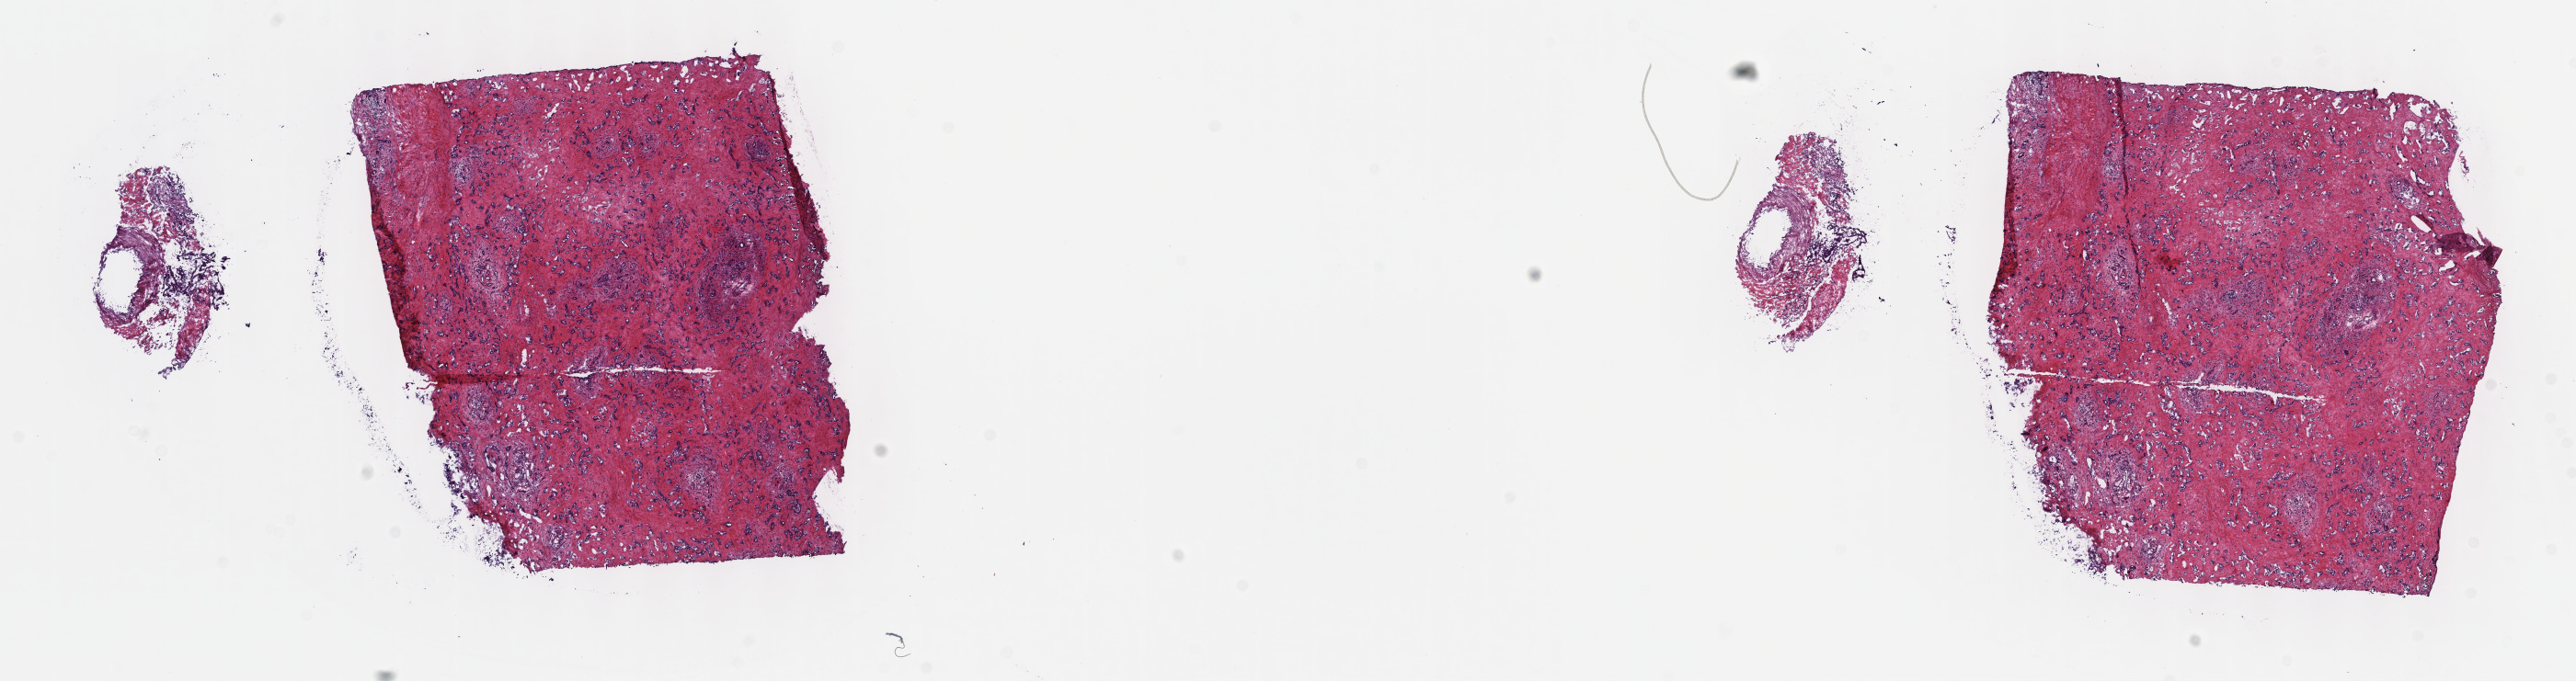
Whole-slide histology image, Hematoxylin and eosin (H&E) stained, shown as a low-resolution overview of the whole scanned area (about 22.7 x 6.0 mm, slide scanned at 40x); frozen section from the top of the tissue portion; bile duct, primary tumour sample. Female patient; age at initial diagnosis 61 years. Histologic grade: G2 (moderately differentiated). Pathologist review of this section (percent, as recorded): tumour cells 100%, tumour nuclei 60%, normal cells 0%, stromal cells 0%, necrosis 0%. Infiltration values recorded for this section: lymphocyte infiltration 3%, monocyte infiltration 0%, neutrophil infiltration 0%.
AJCC pathologic stage: II. Pathologic diagnosis: Cholangiocarcinoma (intrahepatic bile duct).